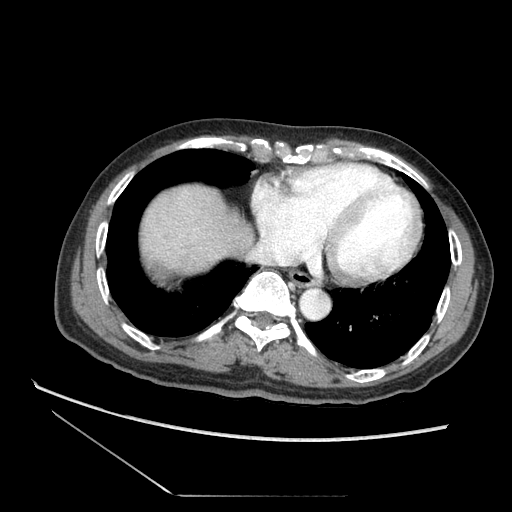
Contrast-enhanced abdominal CT (liver protocol), one axial slice. Position 71 of 73 along the scan axis. Soft-tissue window (W 400 / L 40 HU). 2.5 mm slice thickness. 512 × 512 image matrix, field of view 360 × 360 mm. From the clinical record (not read from this slice): diagnosis: hepatocellular carcinoma (patient treated with transarterial chemoembolisation; whether this scan precedes or follows treatment is not stated here); TNM stage (as recorded): Stage-II; Child-Pugh class: A; tumour differentiation: moderately differentiated; tumour nodularity: multinodular.
Annotated regions visible in this slice (semi-automatically segmented with operator editing):
- abdominal aorta: box from (x=302, y=290) to (x=330, y=318) px
- liver parenchyma outside the tumour (the mass and vessels are separate outlines, so this box may not span the whole liver): (x=132, y=178)–(x=250, y=290)